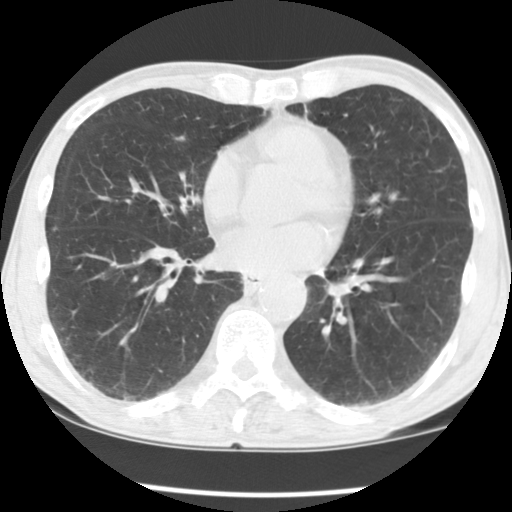
Low-dose screening chest CT, one axial slice; position 58 of 135 along the scan axis; 120 kVp; lung window (W 1500 / L -600 HU); 2.5 mm slice thickness; 512 × 512 image matrix, field of view 310 × 310 mm.
Structures marked on this image (expert manual segmentation):
- lesion 1 (tumor, lower lobe of right lung): box from (x=87, y=367) to (x=97, y=376) px